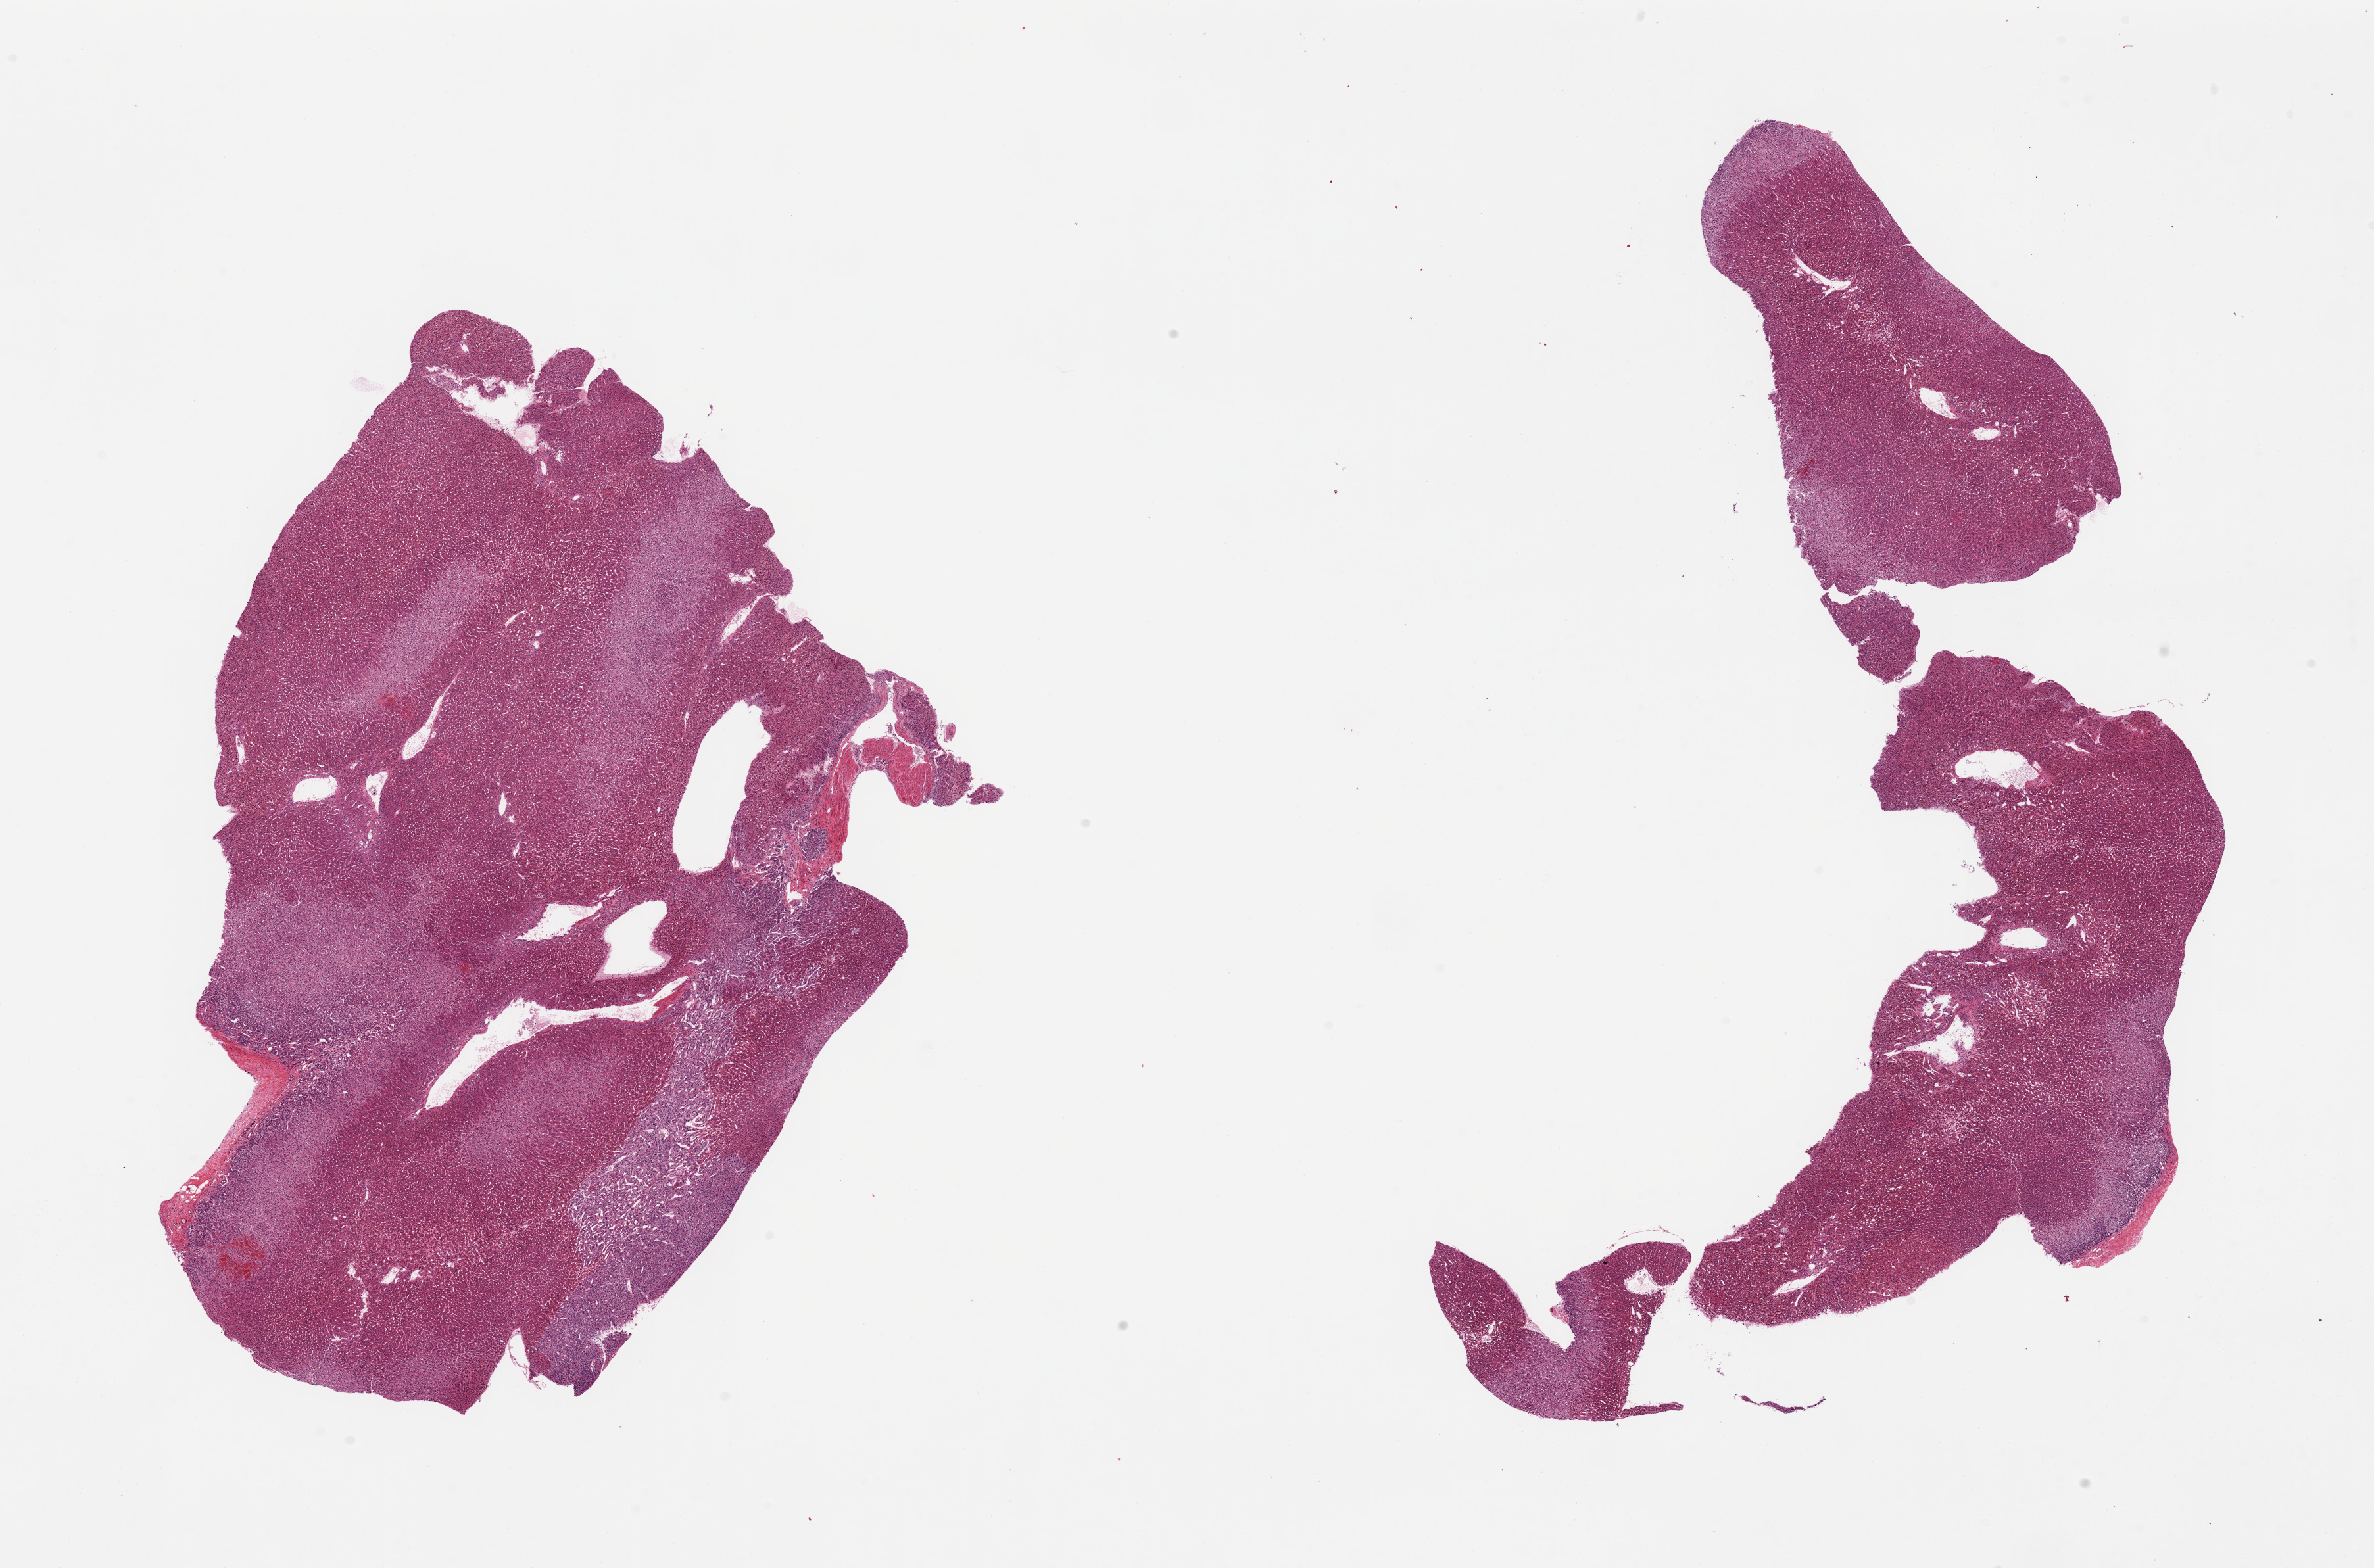
Hematoxylin and eosin (H&E) whole-slide image, brightfield — low-resolution overview of the scanned area, about 28.5 x 18.9 mm, PAXgene-fixed, paraffin-embedded tissue, sampled site (target tissue): adrenal gland, tissue donor sample. Donor: male.
Review note (as recorded): 2 pieces.